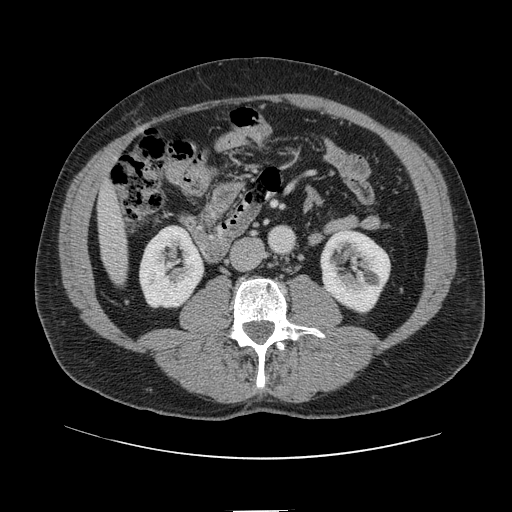
Contrast-enhanced abdominal CT, one axial slice; 120 kVp; soft-tissue window (W 400 / L 40 HU); 2.5 mm slice thickness; 512 × 512 image matrix, field of view 412 × 412 mm. Male patient, age 66 years. Case-level facts recorded for this patient, not image findings: diagnosis: colorectal cancer liver metastases, imaged before liver resection; multiple liver metastases: no; largest metastasis: 3.5 cm.
Outlined on this slice (manually delineated by an expert):
- liver: box from (x=99, y=185) to (x=128, y=285) px
- planned liver remnant (the part of the liver to remain after resection): (x=99, y=186)–(x=123, y=246)